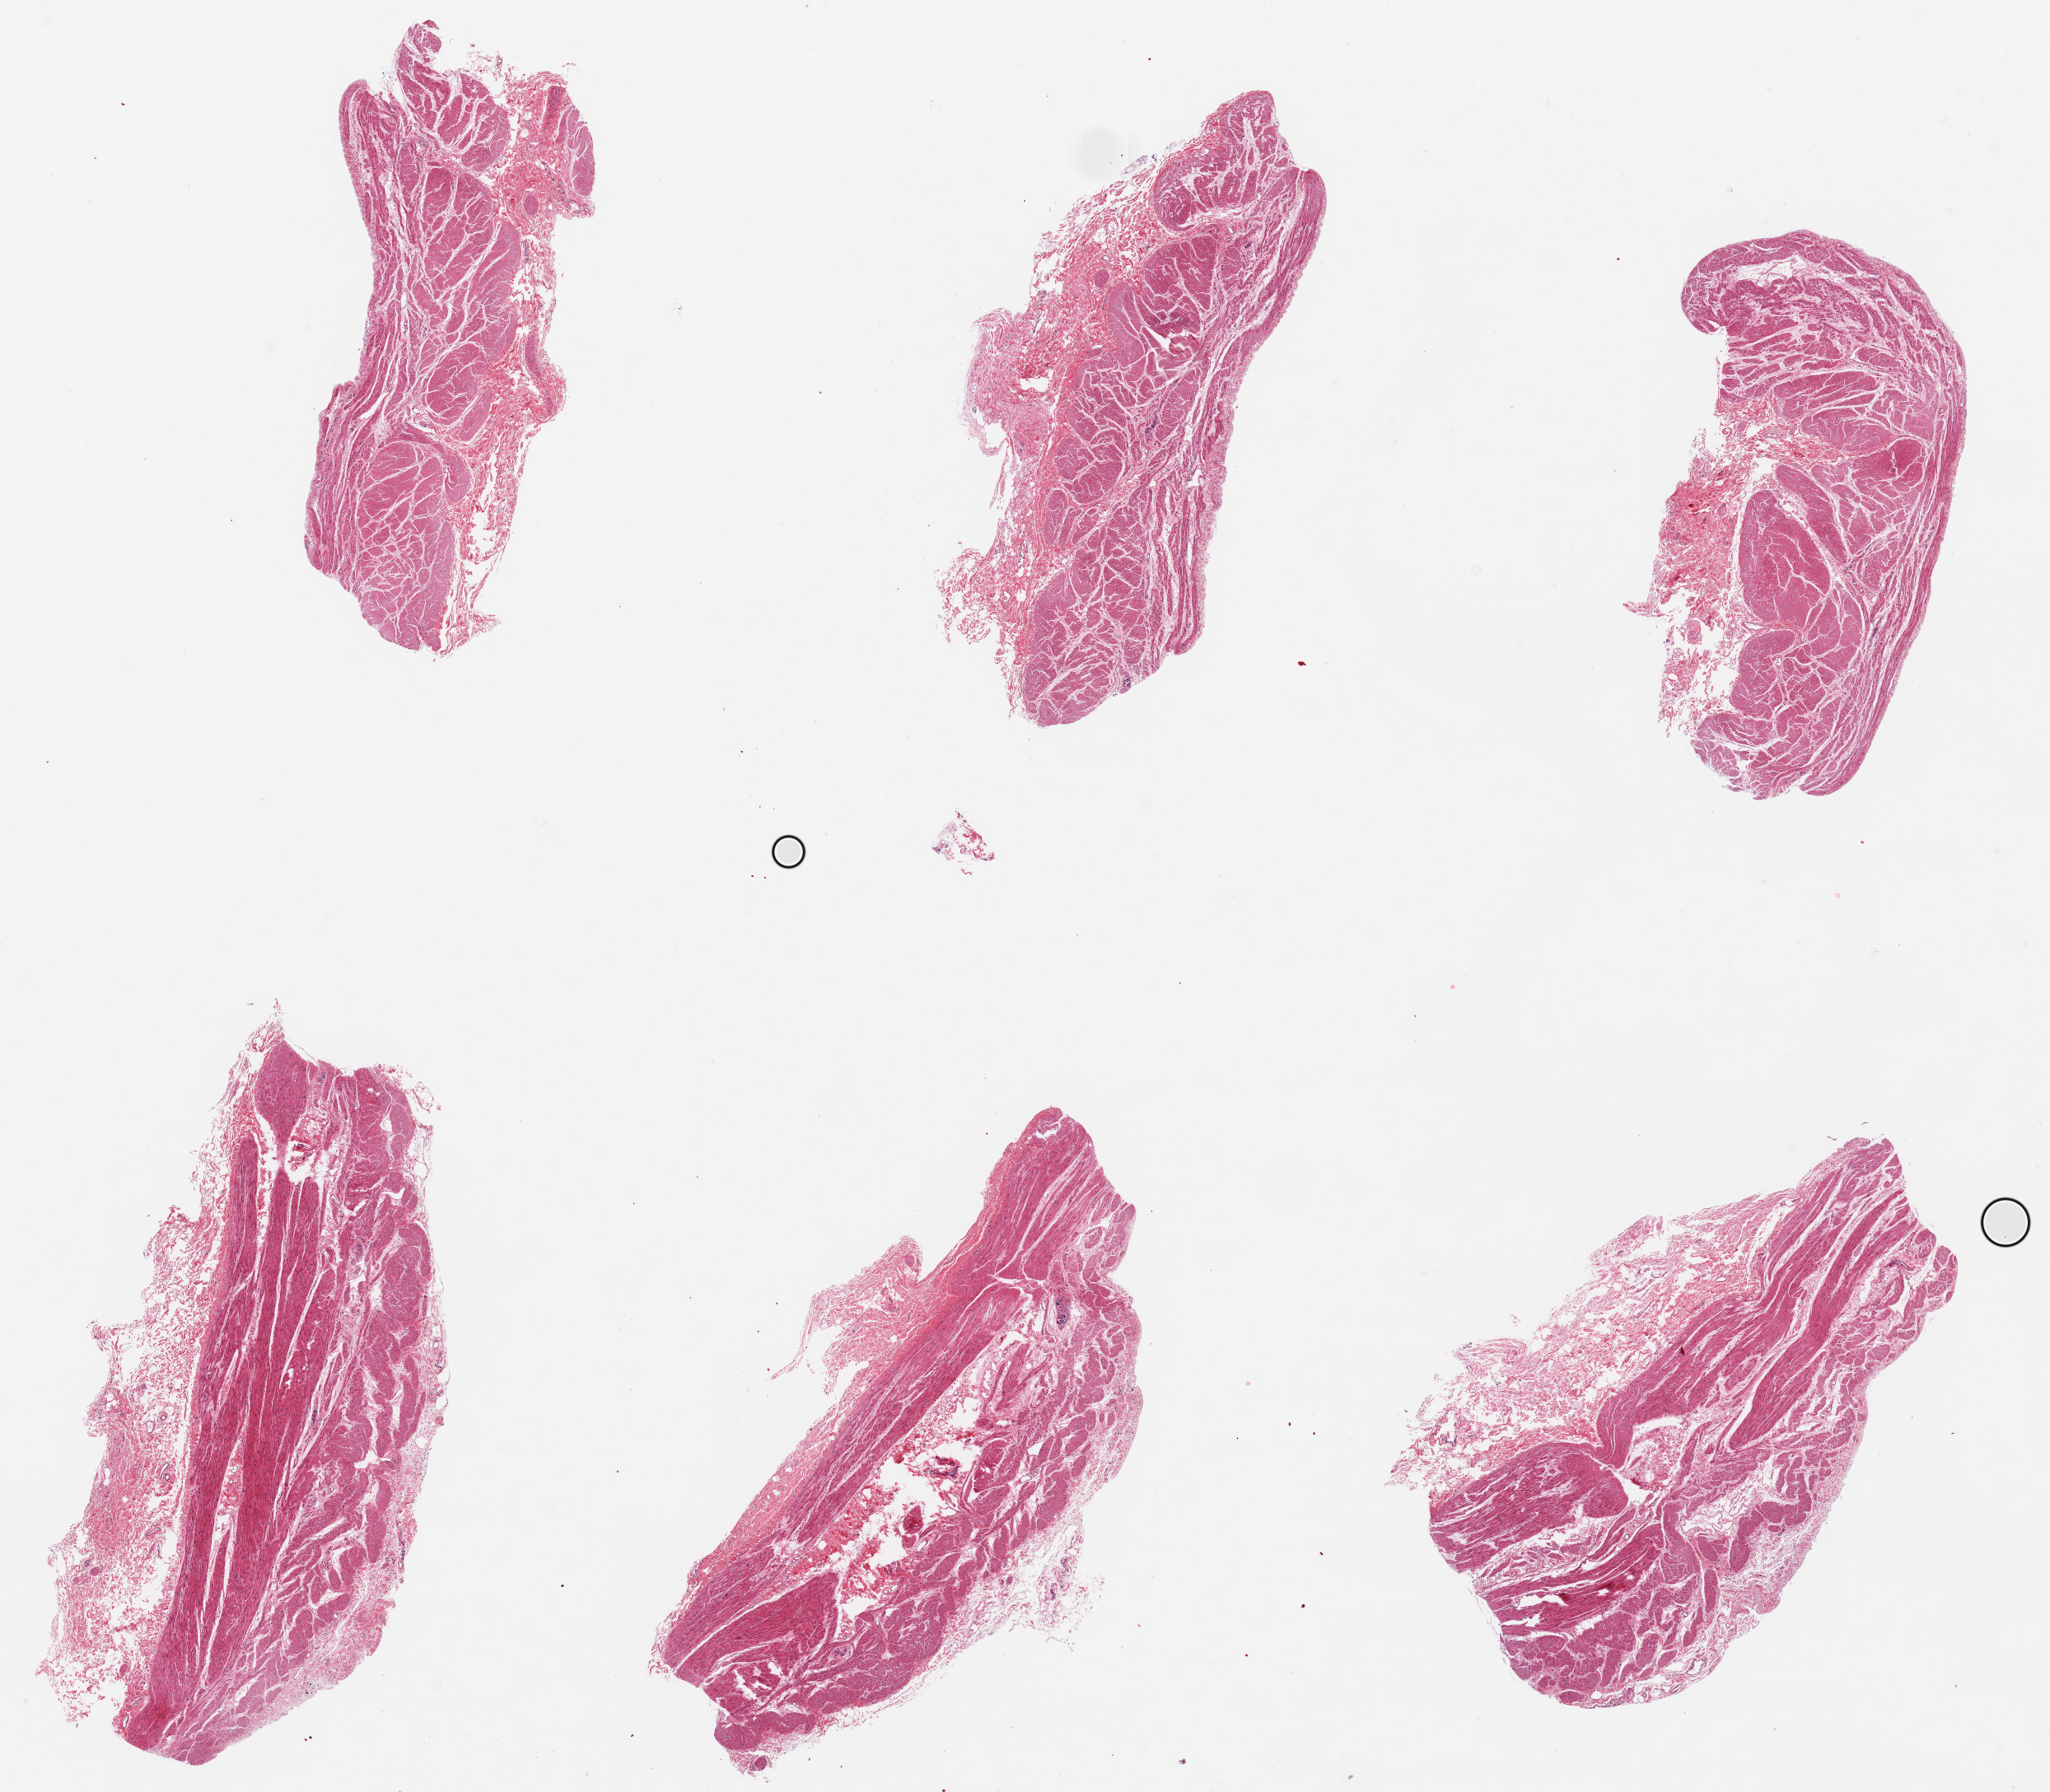
Hematoxylin and eosin (H&E) whole-slide image, brightfield, shown as a low-resolution overview of the whole scanned area (about 19.7 x 17.2 mm). PAXgene-fixed paraffin-embedded (PFPE) section. Target tissue: stomach. Tissue donor sample. Donor: male.
Reviewer comment on this tissue sample: 6 pieces up to ~6x3mm. Muscosa either sloughed or absent, muscualris only.